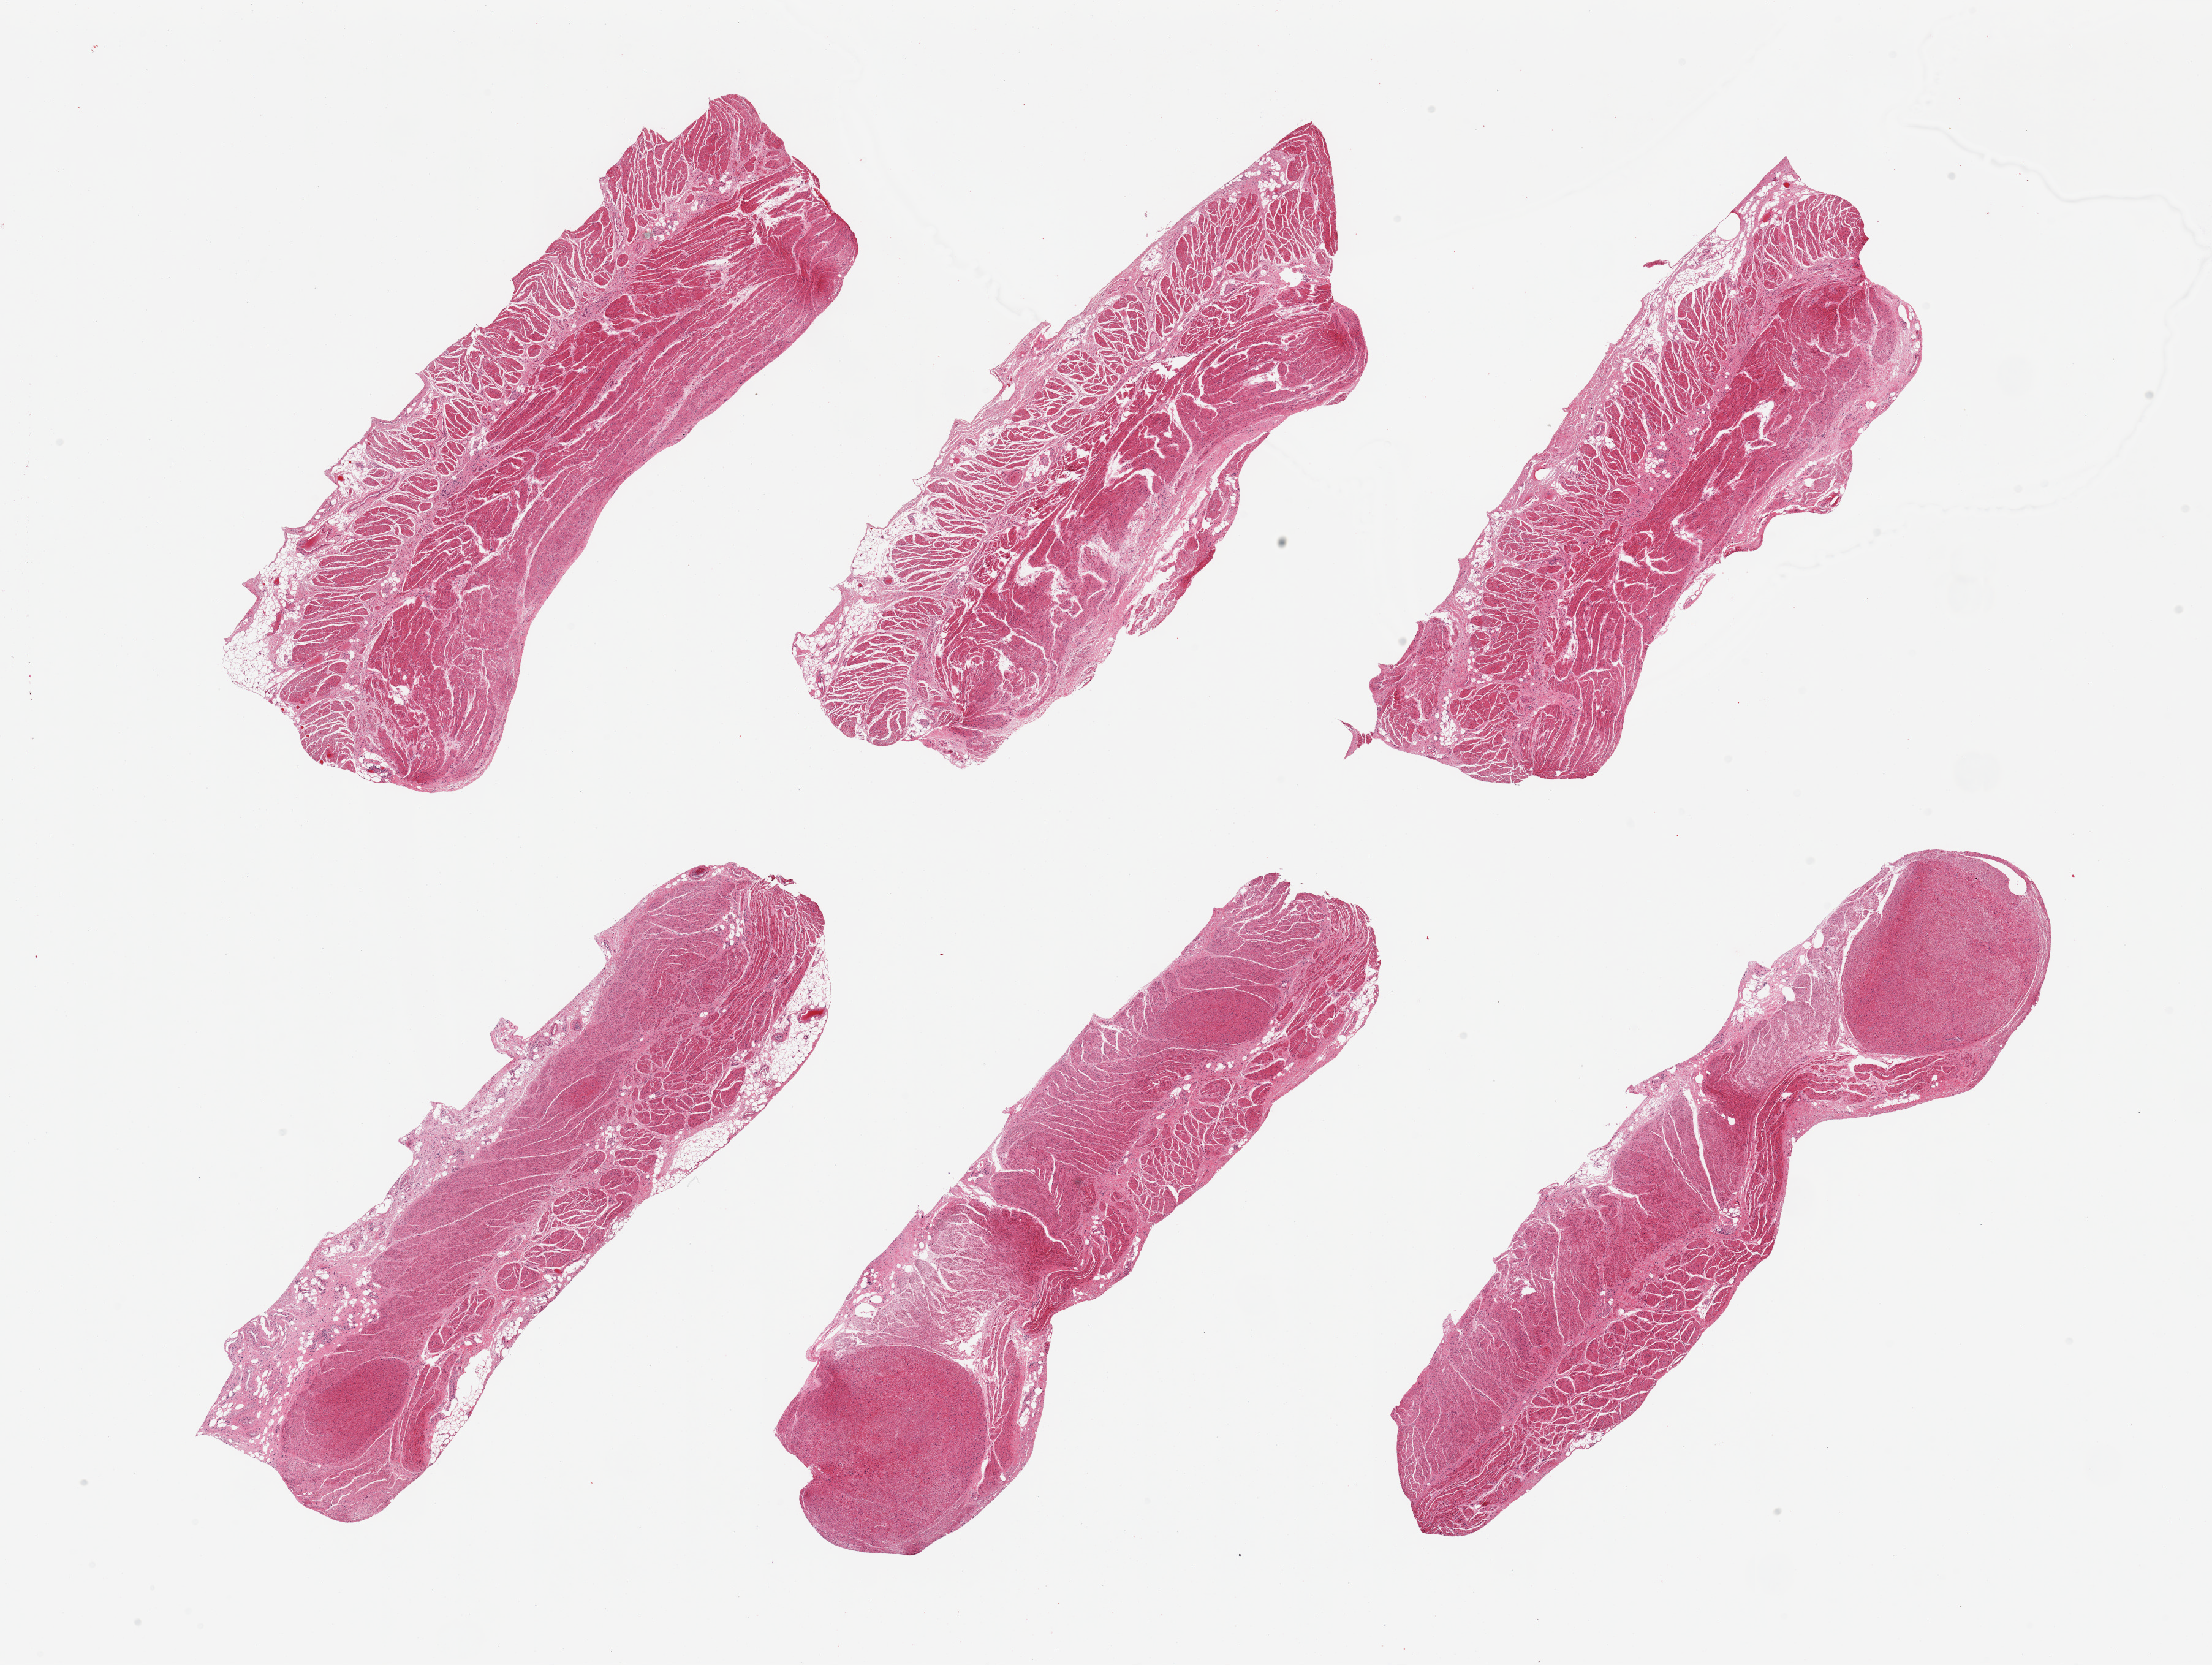
Whole-slide image, haematoxylin and eosin stain, low-resolution overview of the scanned area, about 28.5 x 21.5 mm; PAXgene-fixed, paraffin-embedded tissue; target tissue: gastroesophageal junction; tissue donor sample. Donor sex: male.
Reviewer comment on this tissue sample: 6 pieces; three pieces contain small leiomyoma.